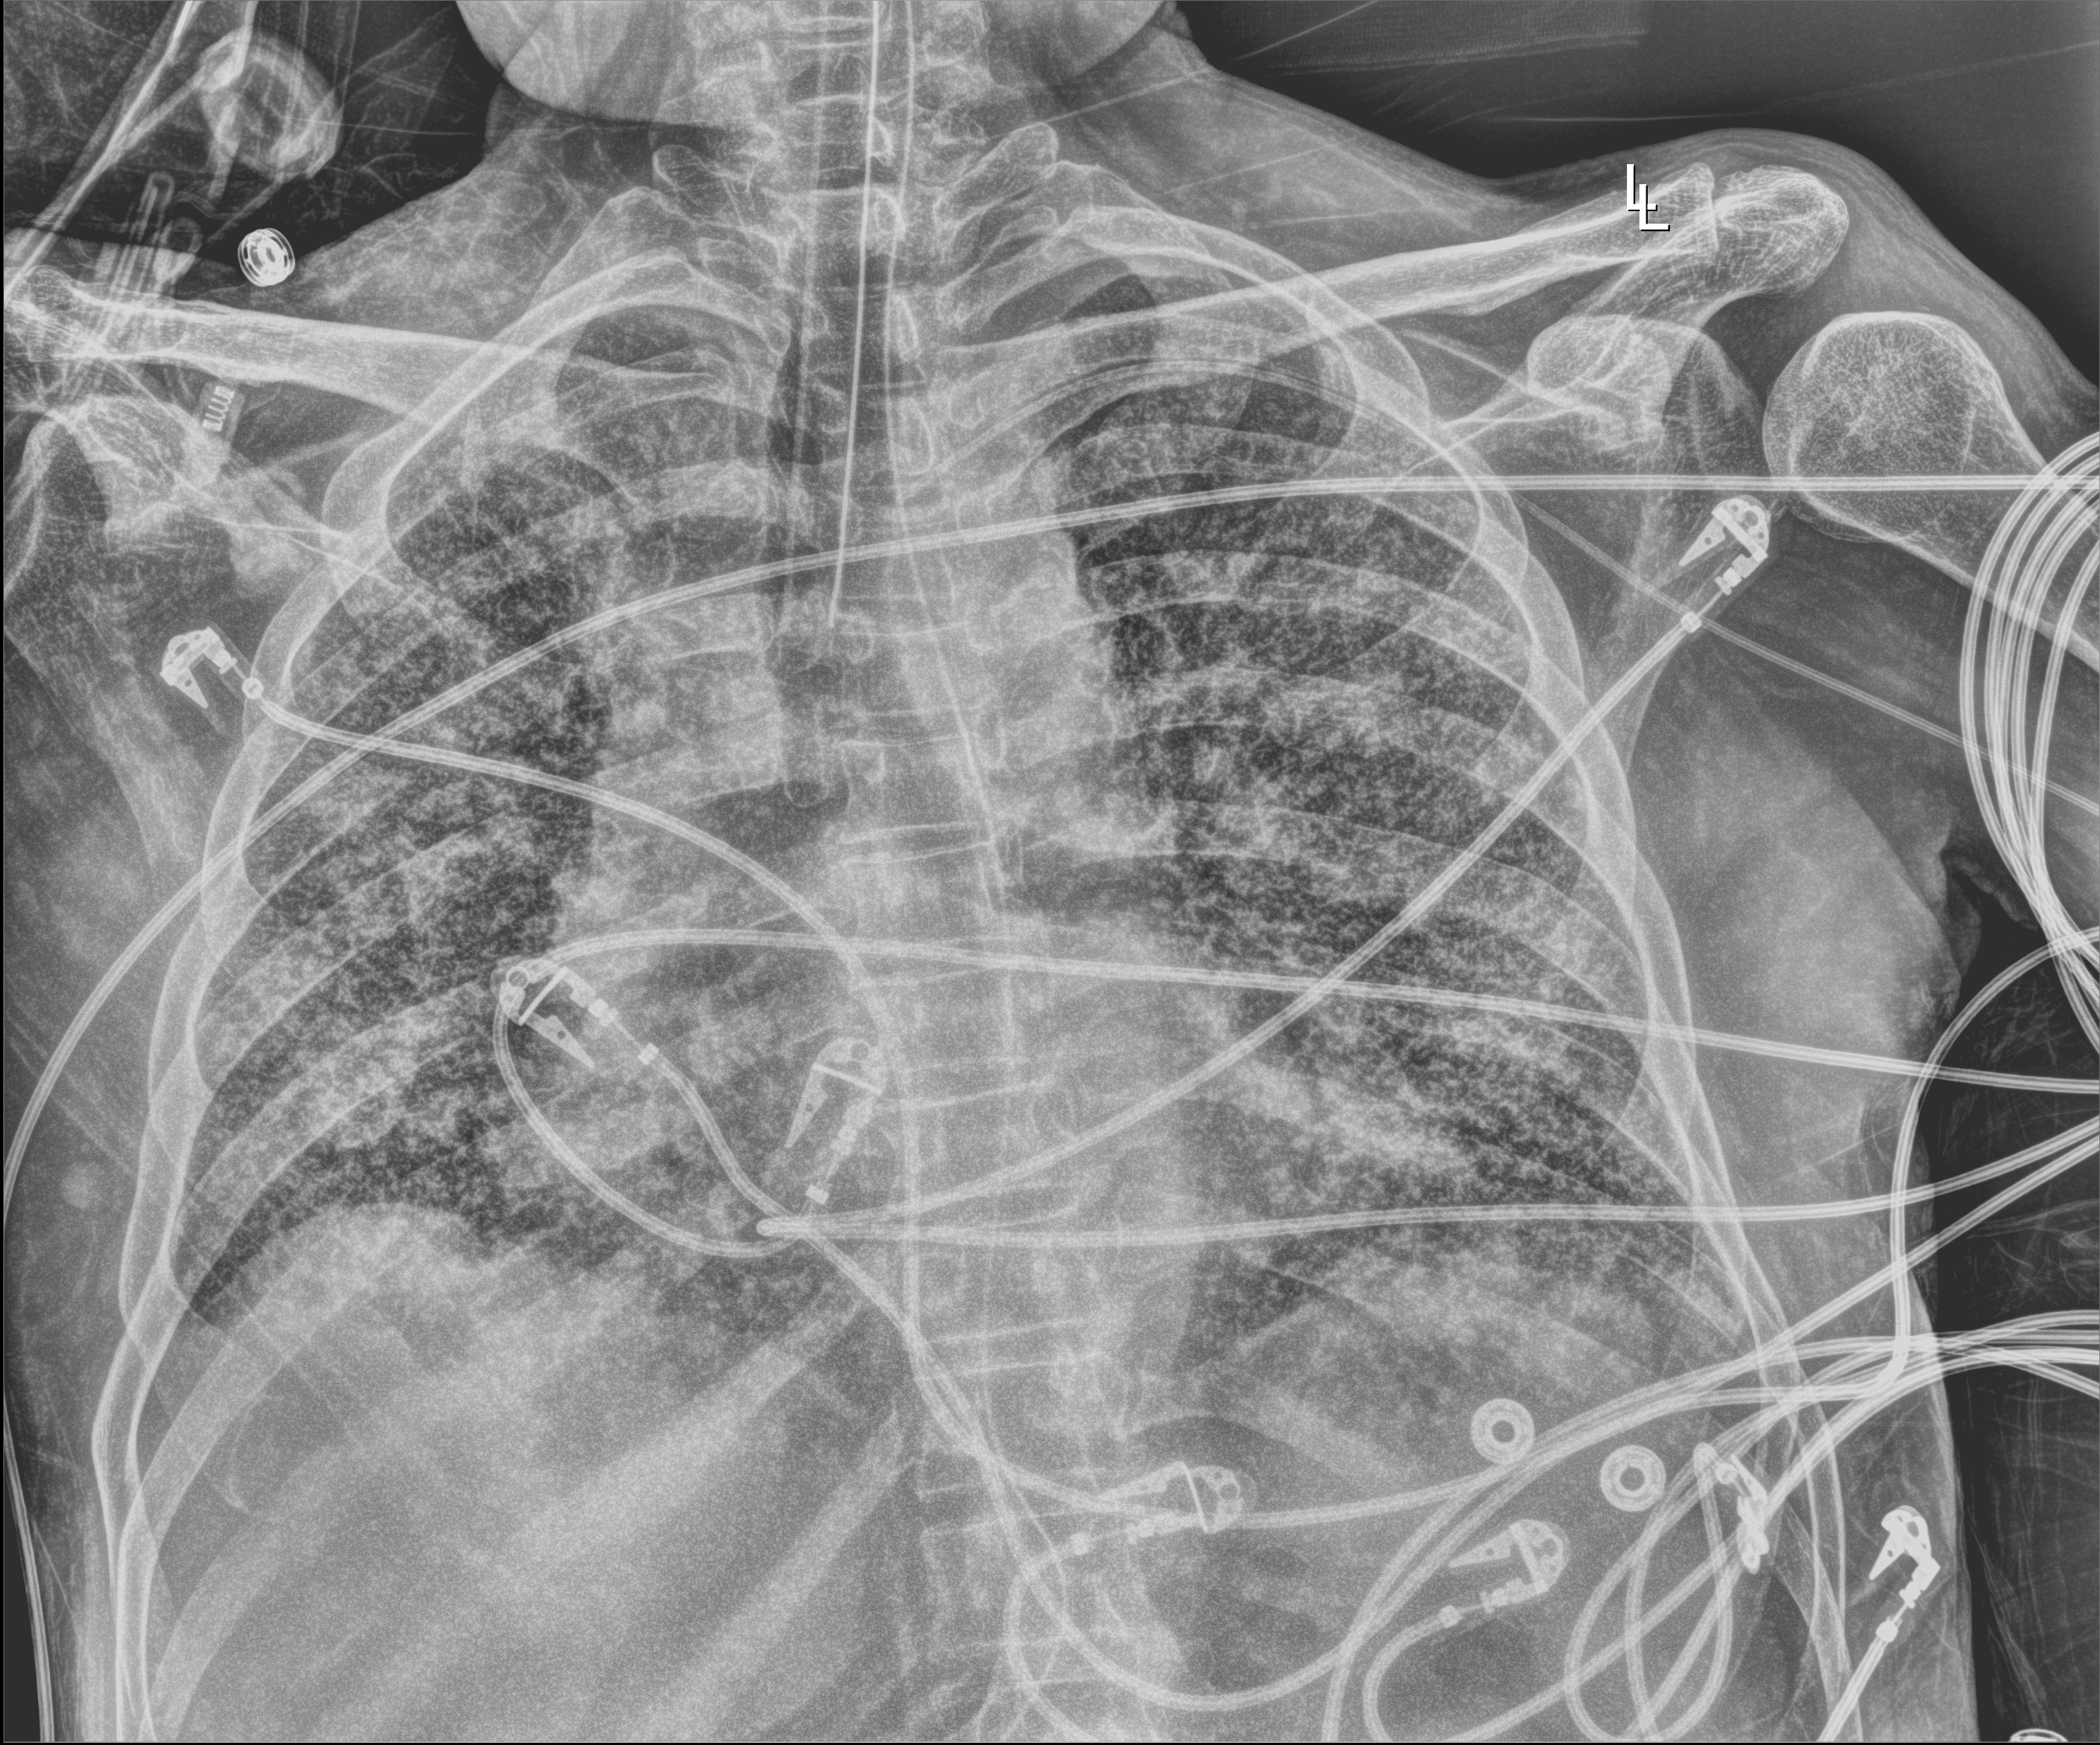
Chest X-ray. Patient hospitalised with COVID-19; male, aged 60–74 years.
Admission-level facts for this patient (not findings on this image; timing relative to this image not recorded): length of hospital stay: 54 days.